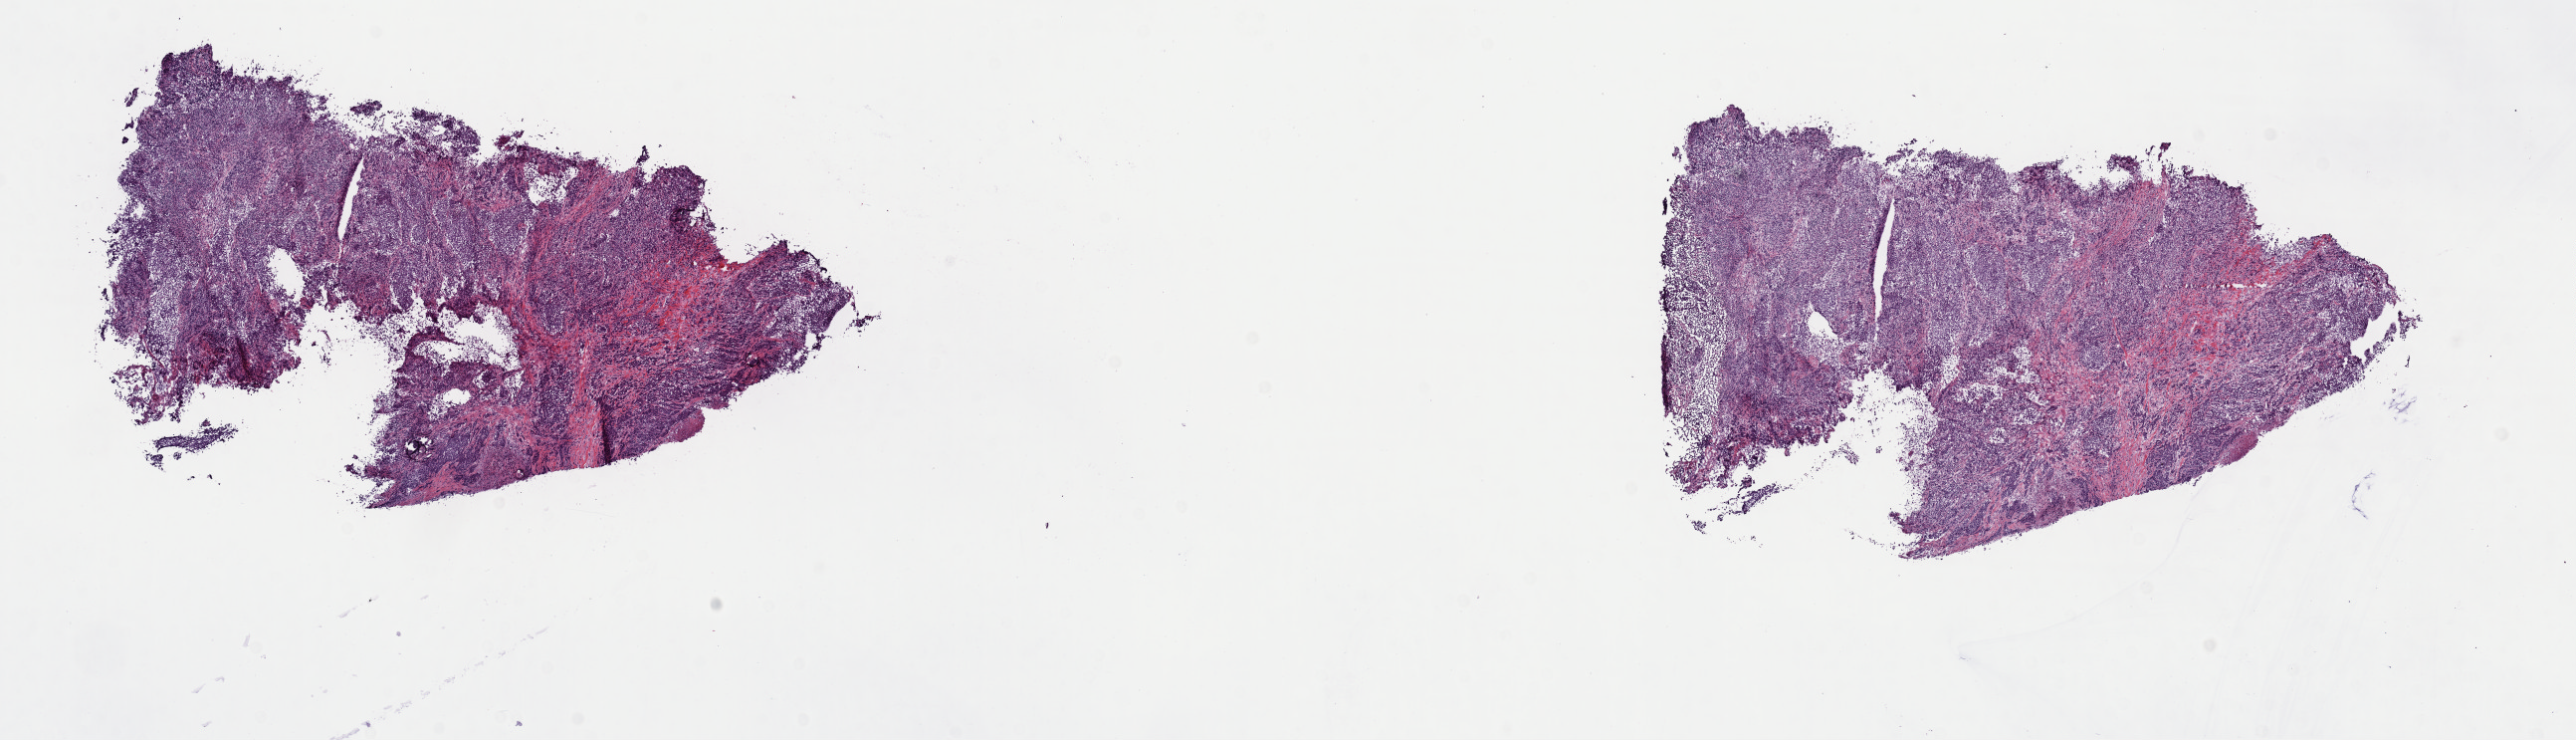
Digitized Hematoxylin and eosin (H&E) stained tissue section (whole slide) — shown as a low-resolution overview of the whole scanned area (about 20.4 x 5.9 mm, acquisition: 40x scan). Frozen section from the top of the tissue portion. Primary tumour sample from the lung. Male, age 53 years at initial diagnosis. Pathologist review of this section (percent, as recorded): tumour cells 40%, tumour nuclei 70%, normal cells 10%, stromal cells 30%, necrosis 20%. Inflammatory infiltration, as recorded: lymphocyte infiltration 12%, monocyte infiltration 3%, neutrophil infiltration 0%.
- diagnosis: Squamous cell carcinoma, NOS
- AJCC pathologic stage: IIA